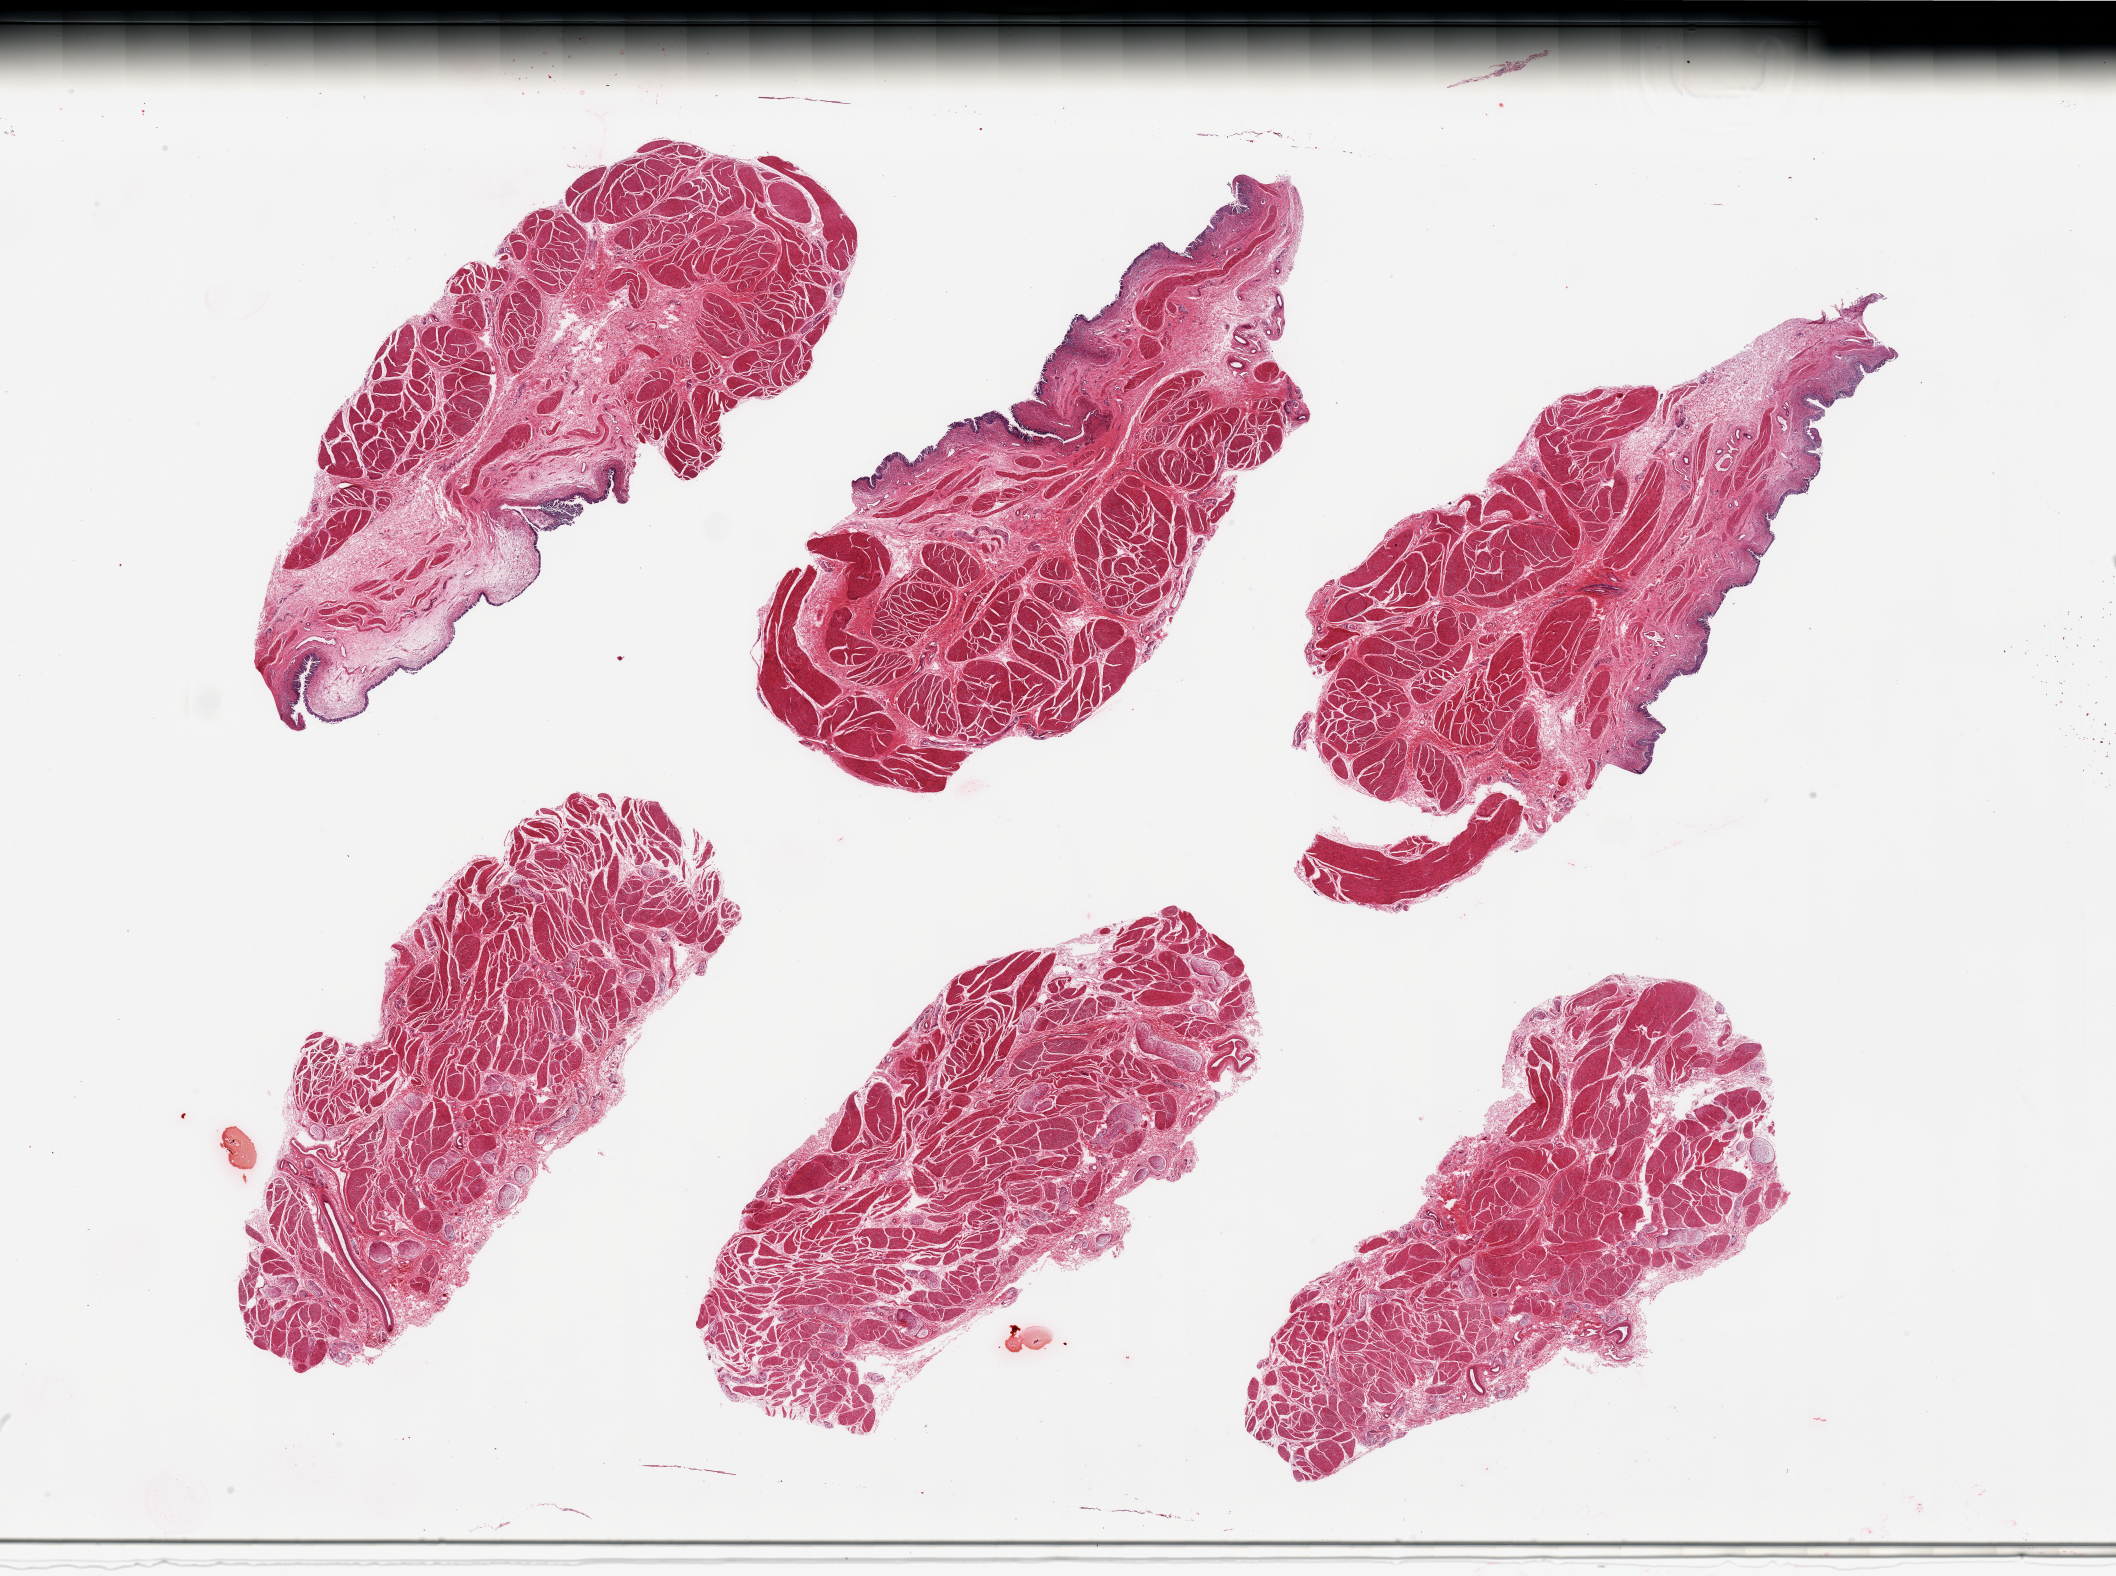
H&E whole-slide image, whole scanned area (about 33.5 x 24.9 mm) shown as a low-resolution overview; PAXgene-fixed paraffin-embedded (PFPE) section; sampled site (target tissue): vagina; donor tissue sample. Donor sex: female.
Review note (as recorded): 6 pieces; bladder, not vagina.